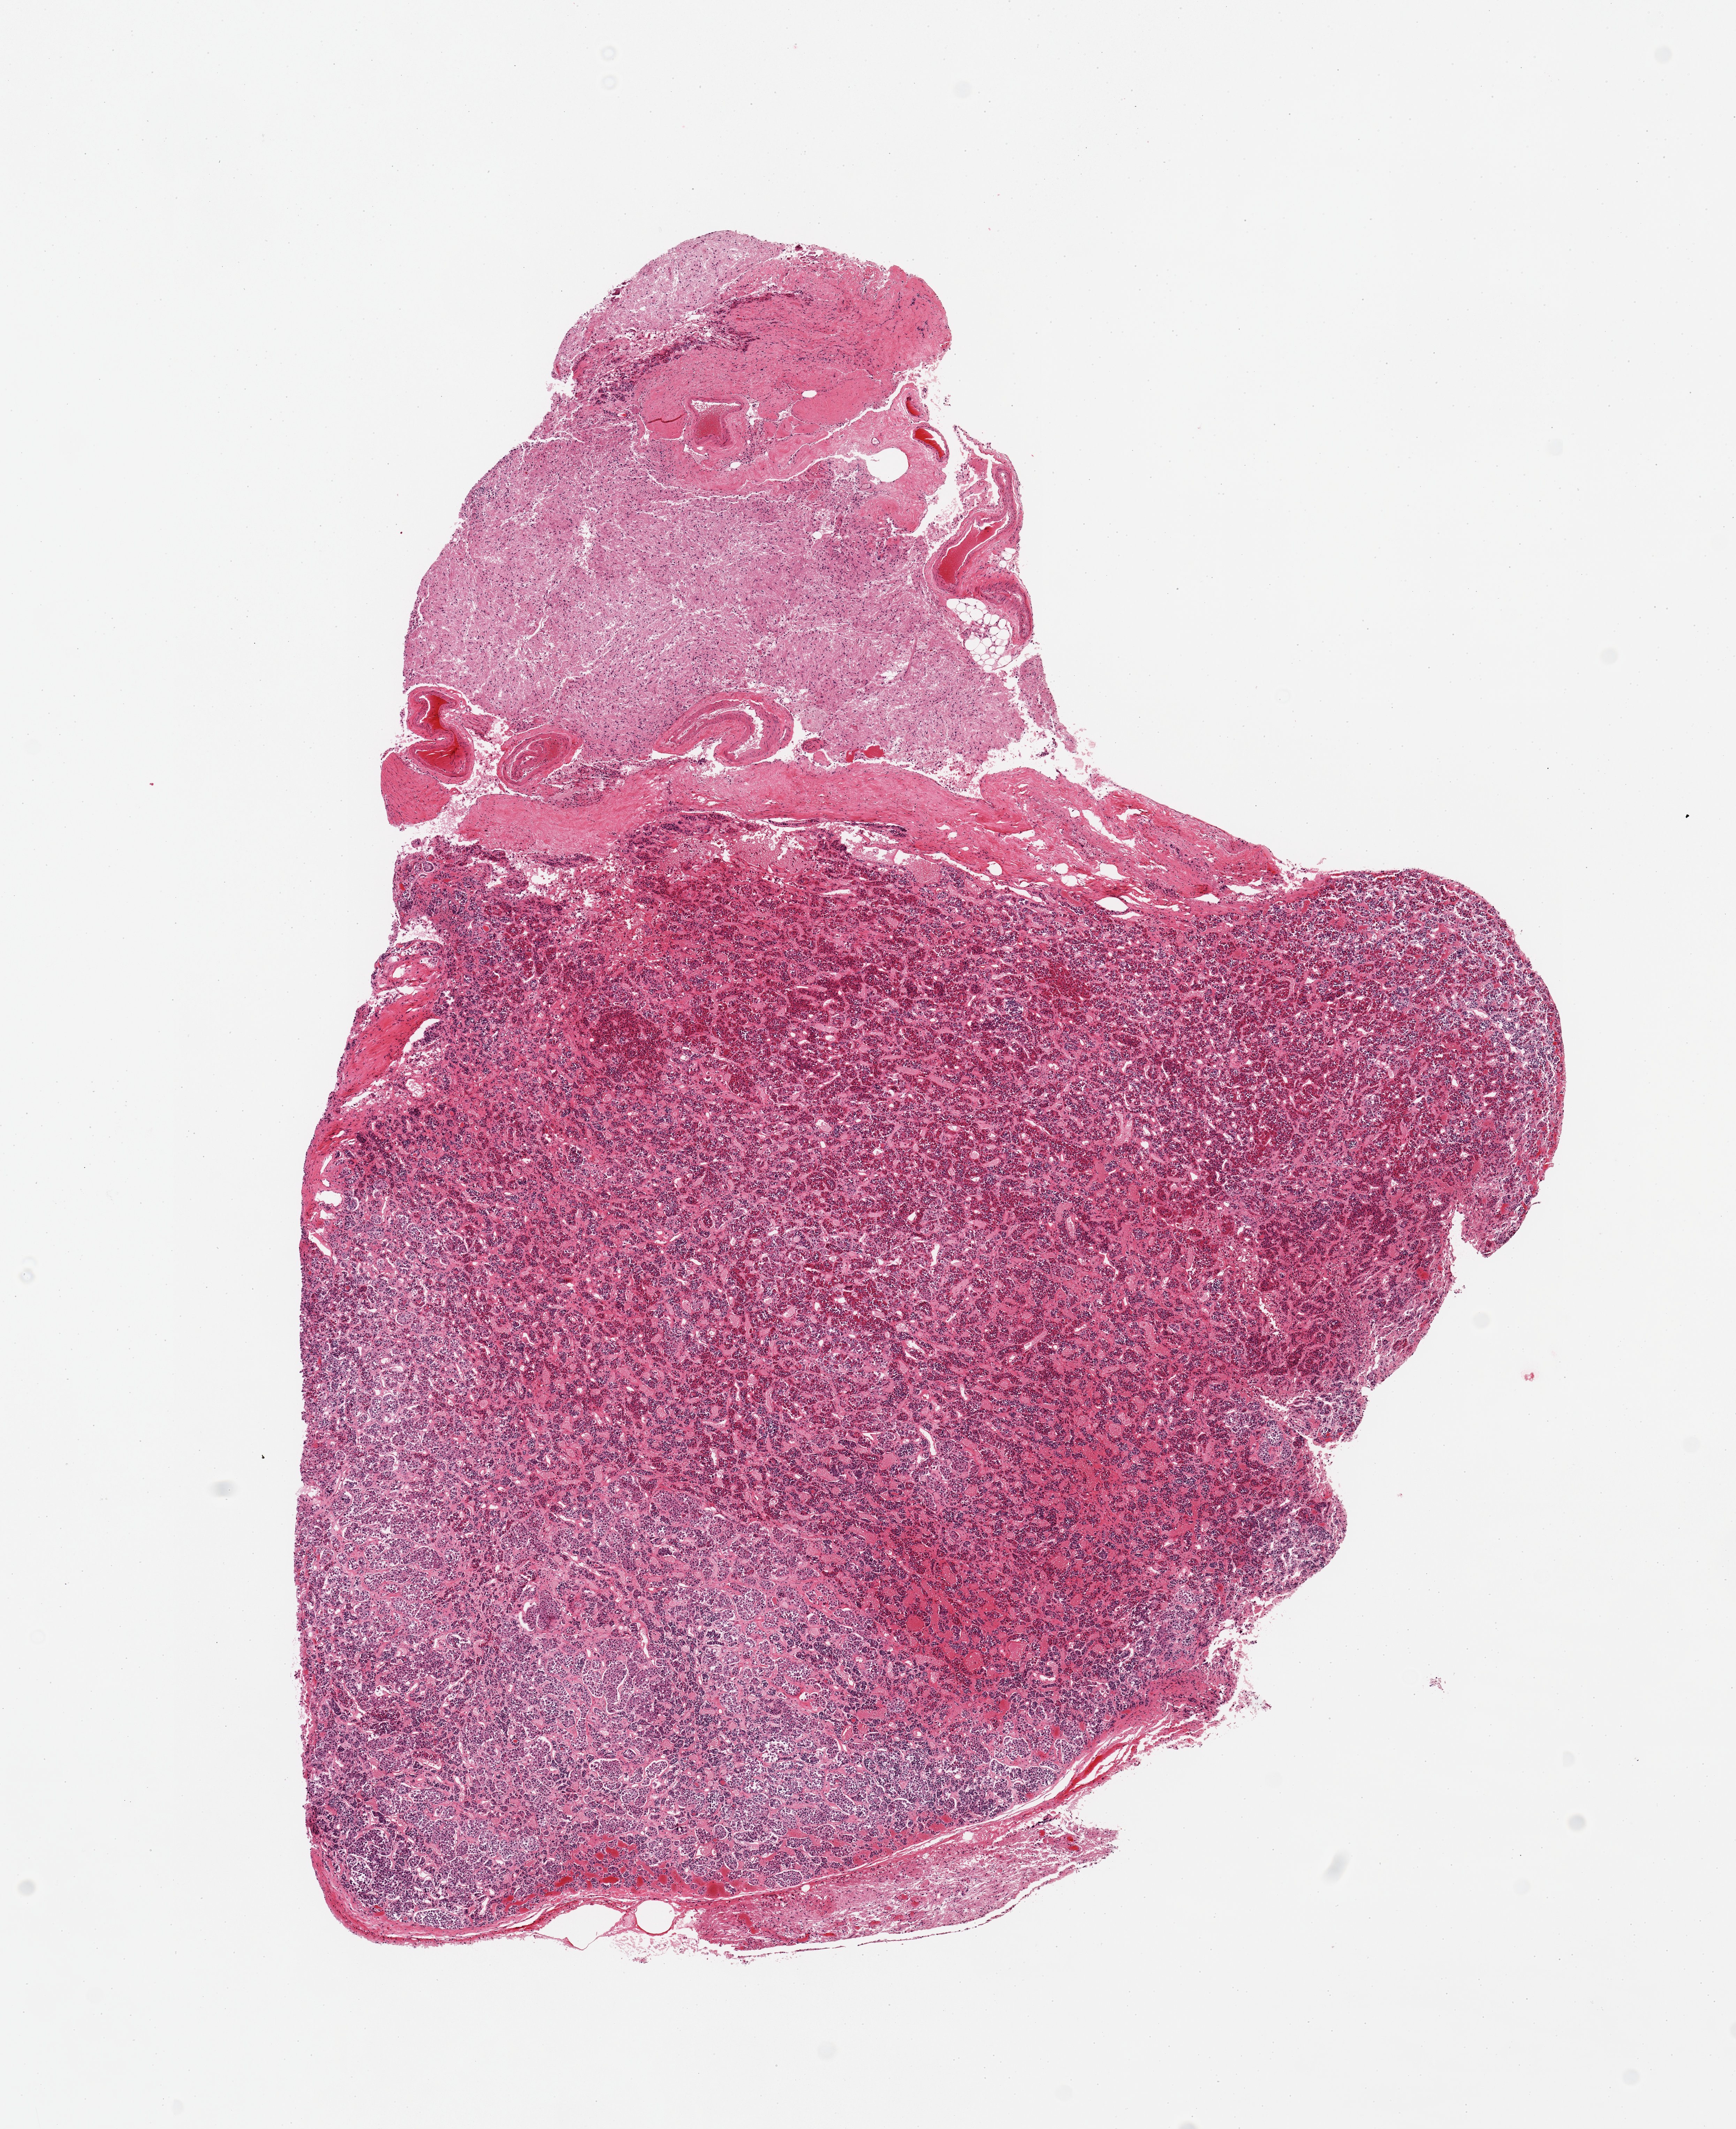
Haematoxylin and eosin whole-slide image, low-resolution overview of the scanned area, about 9.8 x 12.1 mm; PAXgene-fixed paraffin-embedded (PFPE) section; target tissue: pituitary; donor tissue sample. Male donor.
- pathologist's review note for this sample: 1 piece; posterior and anterior present